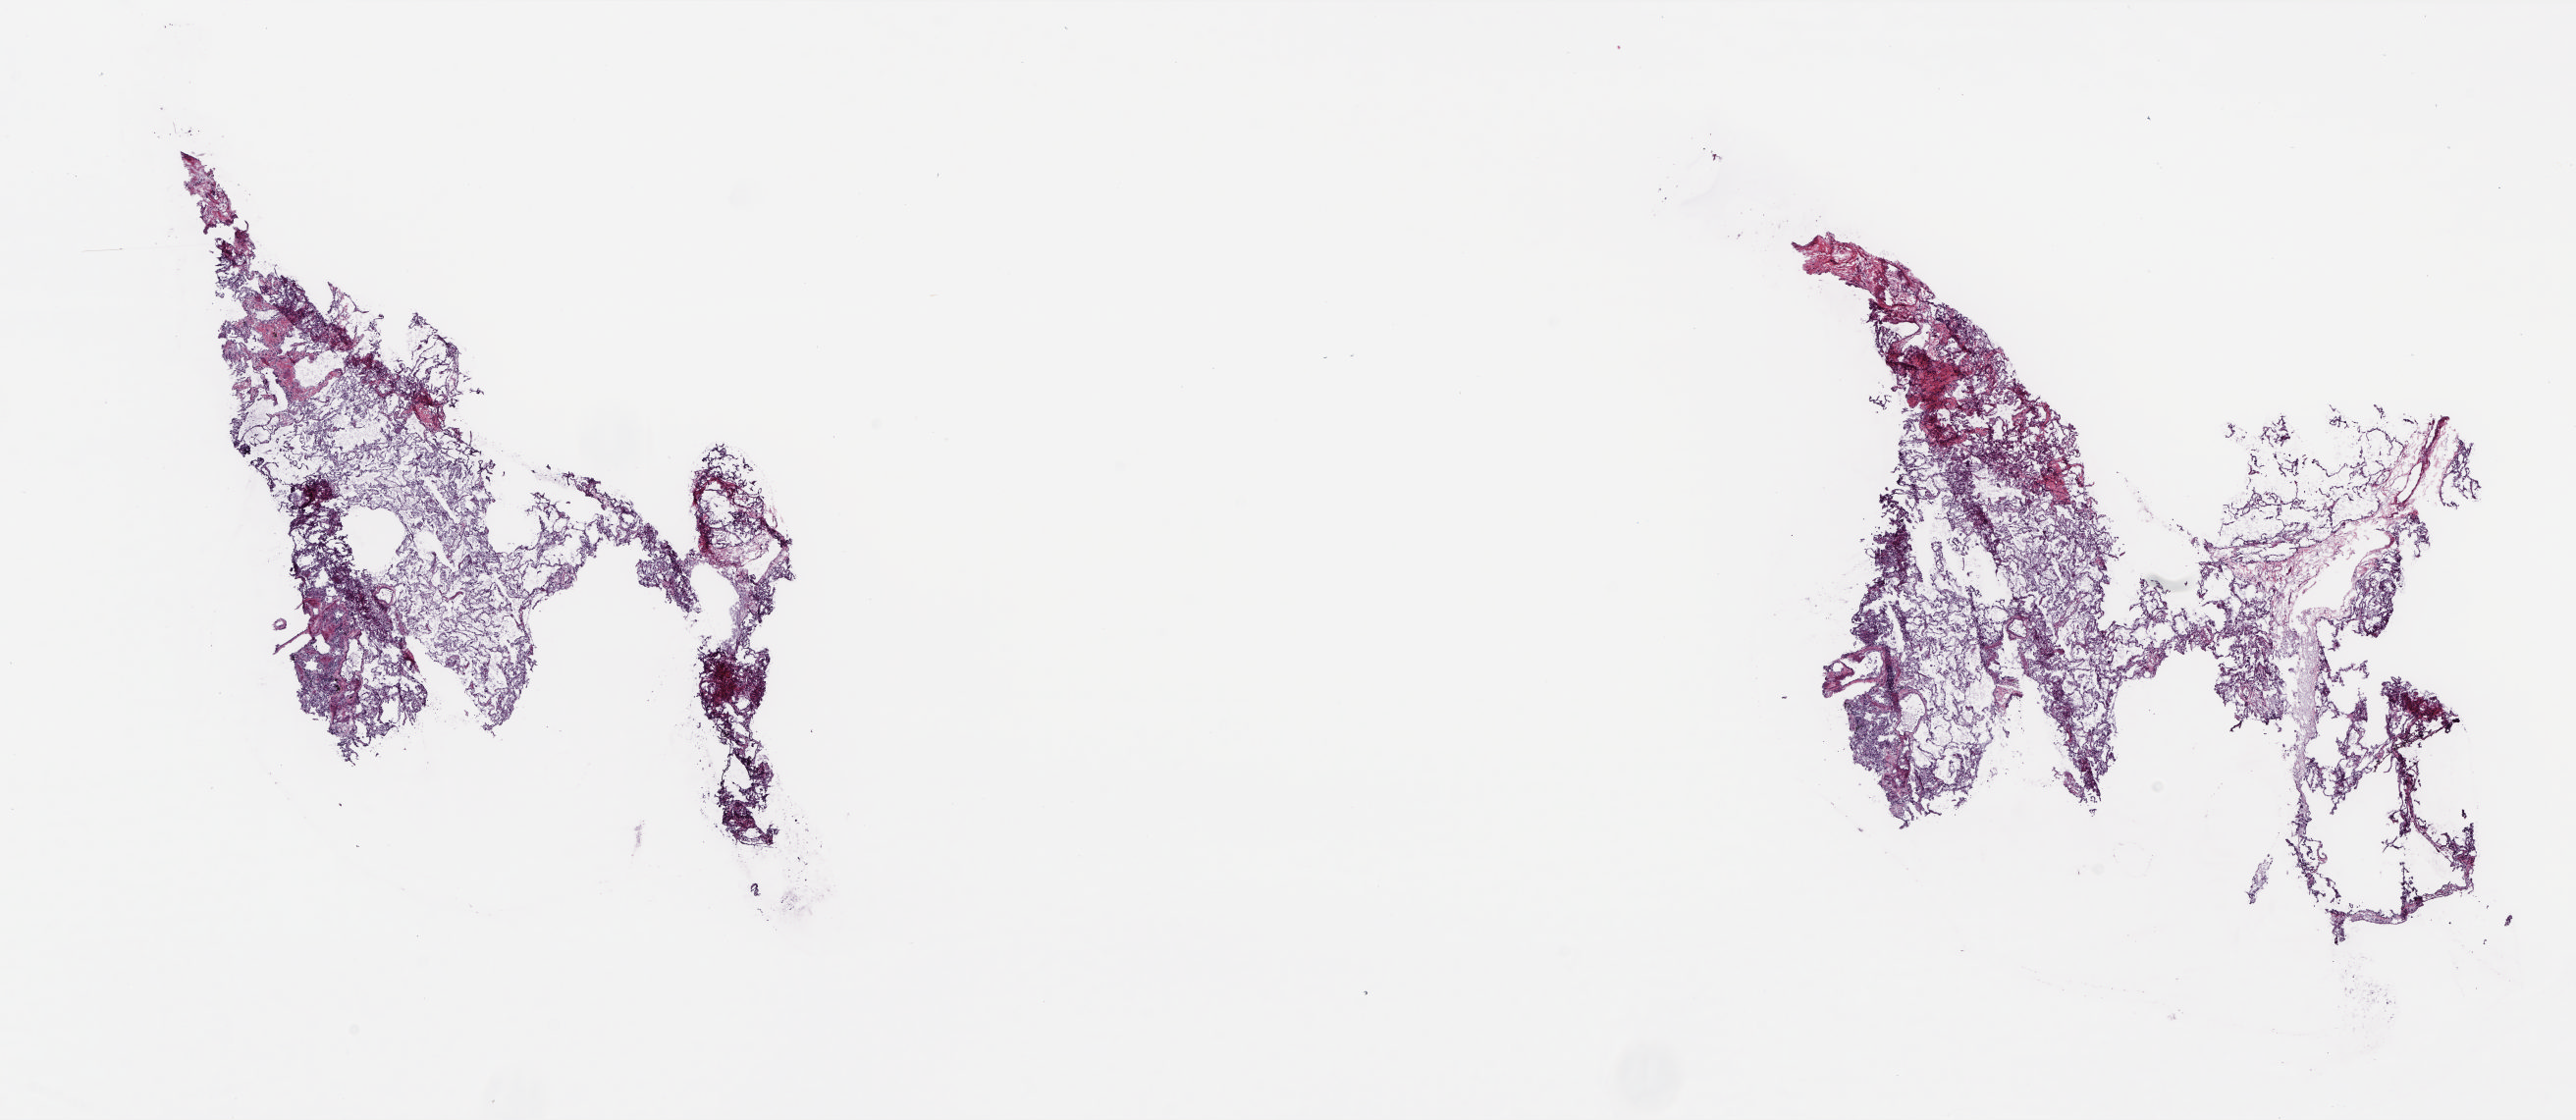
H&E-stained whole-slide image, a low-resolution overview of the entire scanned area, about 21.2 x 9.2 mm; frozen section from the top of the tissue portion; solid tissue normal (non-tumour tissue) sample from the lung. Female patient; age at initial diagnosis 67 years. Pathologist review of this section (percent, as recorded): tumour cells 0%, tumour nuclei 0%, normal cells 100%, stromal cells 0%, necrosis 0%. Inflammatory infiltration, as recorded: lymphocyte infiltration 5%, monocyte infiltration 10%, neutrophil infiltration 1%.
This section: solid tissue normal sample (biorepository sample class). Patient diagnosis: Adenocarcinoma, NOS (upper lobe, lung).